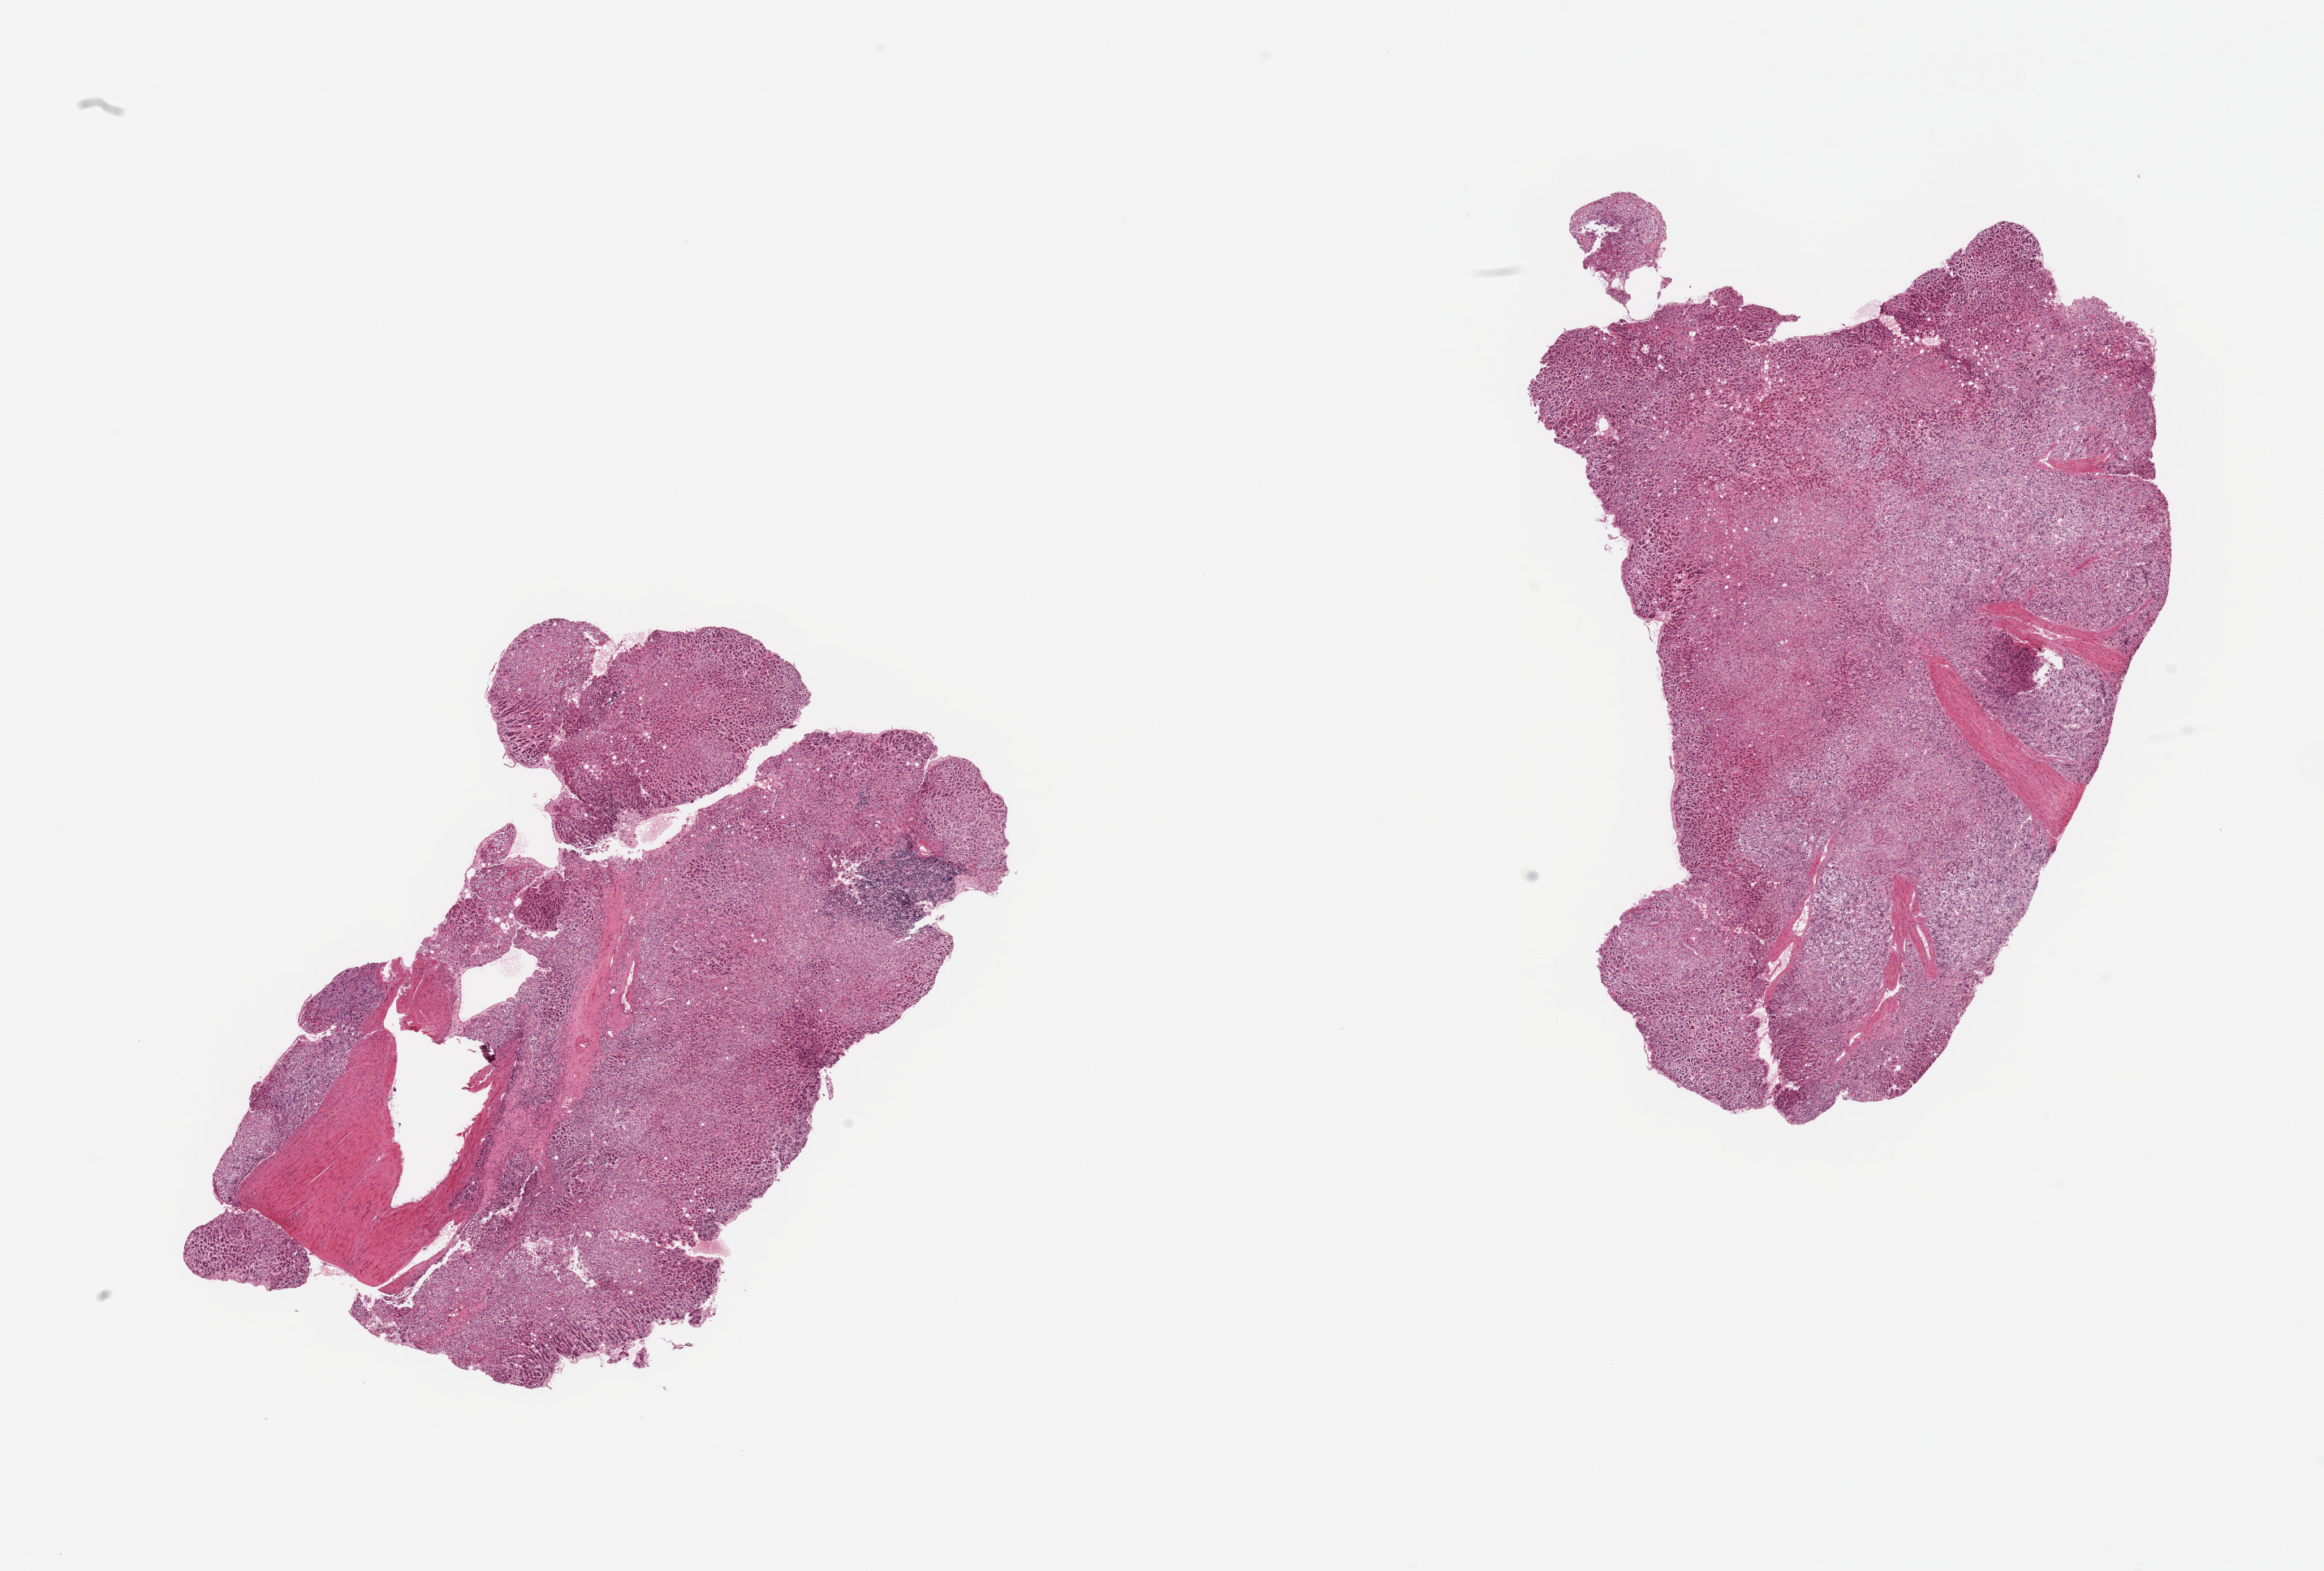
Digitized haematoxylin and eosin-stained section, brightfield, a low-resolution overview of the entire scanned area, about 22.6 x 15.3 mm. PAXgene-fixed paraffin-embedded (PFPE) section. Target tissue: adrenal gland. Tissue donor sample. Male donor.
• review note (as recorded): 2 pieces; atypical lymphoid infiltrate